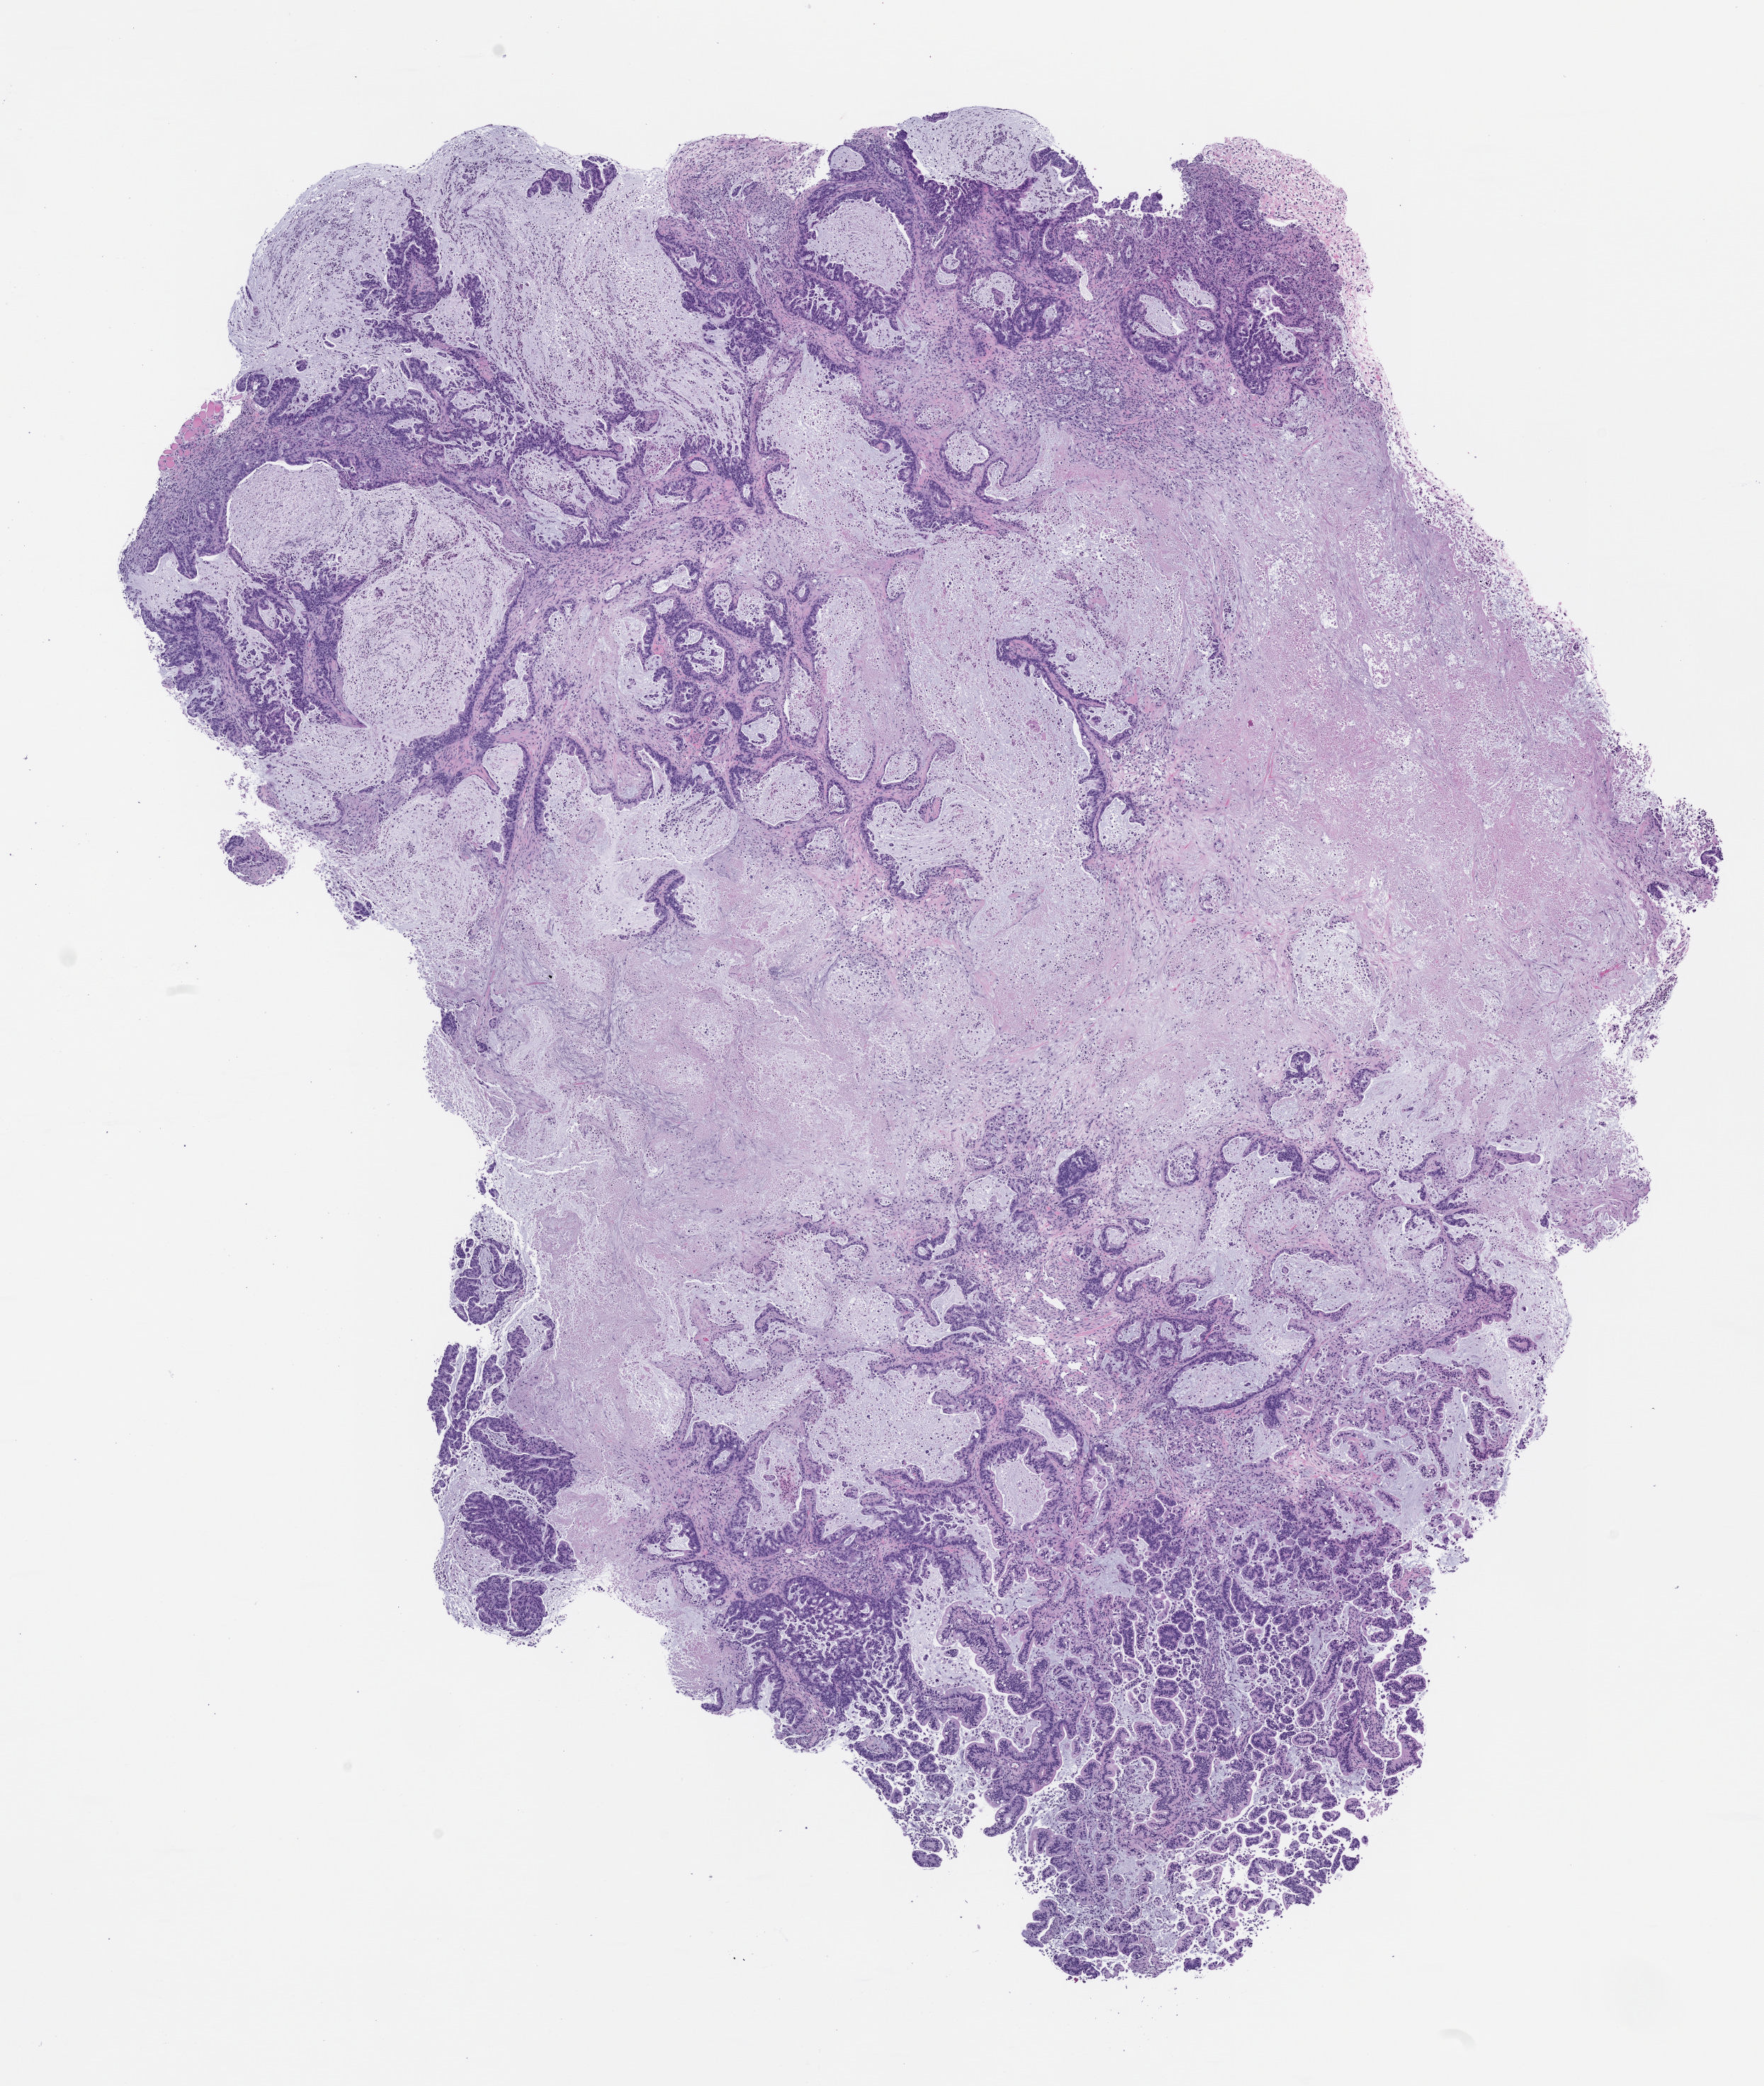
Whole-slide image, haematoxylin and eosin: patient-derived xenograft (human tumor grown in a mouse), passage 0 — shown as a low-resolution overview of the whole scanned area (about 10.0 x 11.8 mm). Formalin-fixed, paraffin-embedded (FFPE) tissue. Tumor site category: pancreas.
Originating patient diagnosis: Pancreatic Adenocarcinoma.